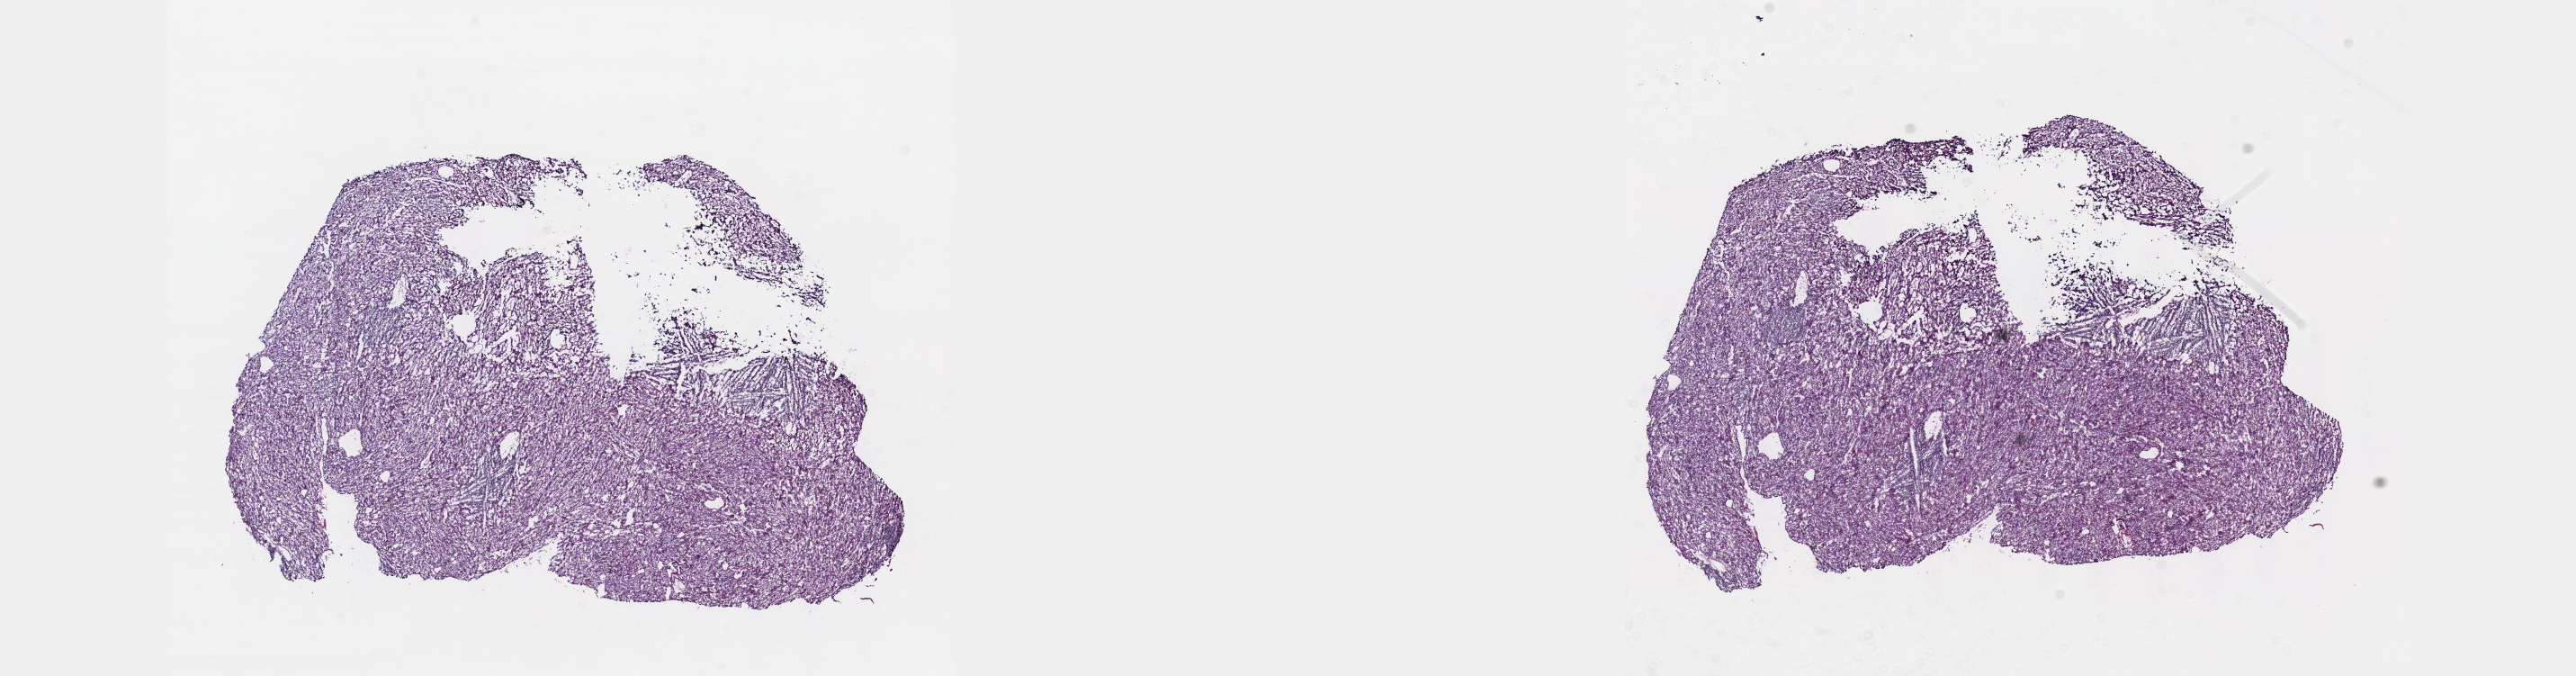
Whole-slide histology image, Hematoxylin and eosin (H&E) stained — a low-resolution overview of the entire scanned area, about 23.1 x 6.1 mm. Frozen section. Thymus, primary tumour sample. Male, age 61 years at initial diagnosis. Slide review estimates, as recorded: tumour cells 99%, tumour nuclei 99%, normal cells 0%, stromal cells 1%, necrosis 0%. Inflammatory infiltration, as recorded: lymphocyte infiltration 0%, monocyte infiltration 0%, neutrophil infiltration 0%.
Pathologic diagnosis: Thymoma, type AB, malignant.